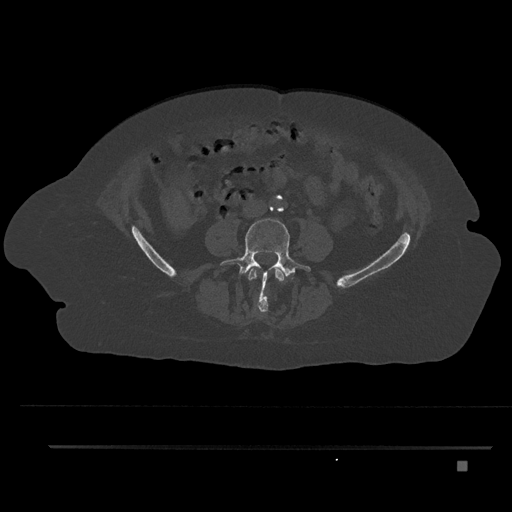
CT including the spine, one axial slice; slice 90 of 797 in the series (ordered by position); bone window (W 1800 / L 400 HU); 0.5 mm slice thickness; 512 × 512 image matrix. Female patient, age 76 years. Case-level facts recorded for this patient, not image findings: primary cancer: lung.
Structures marked on this image (semi-automatic segmentation, software-assisted and operator-edited):
- L3 vertebra: bounding box <248,267,285,313> (left, top, right, bottom; pixels)
- L4 vertebra: <220,218,311,301>